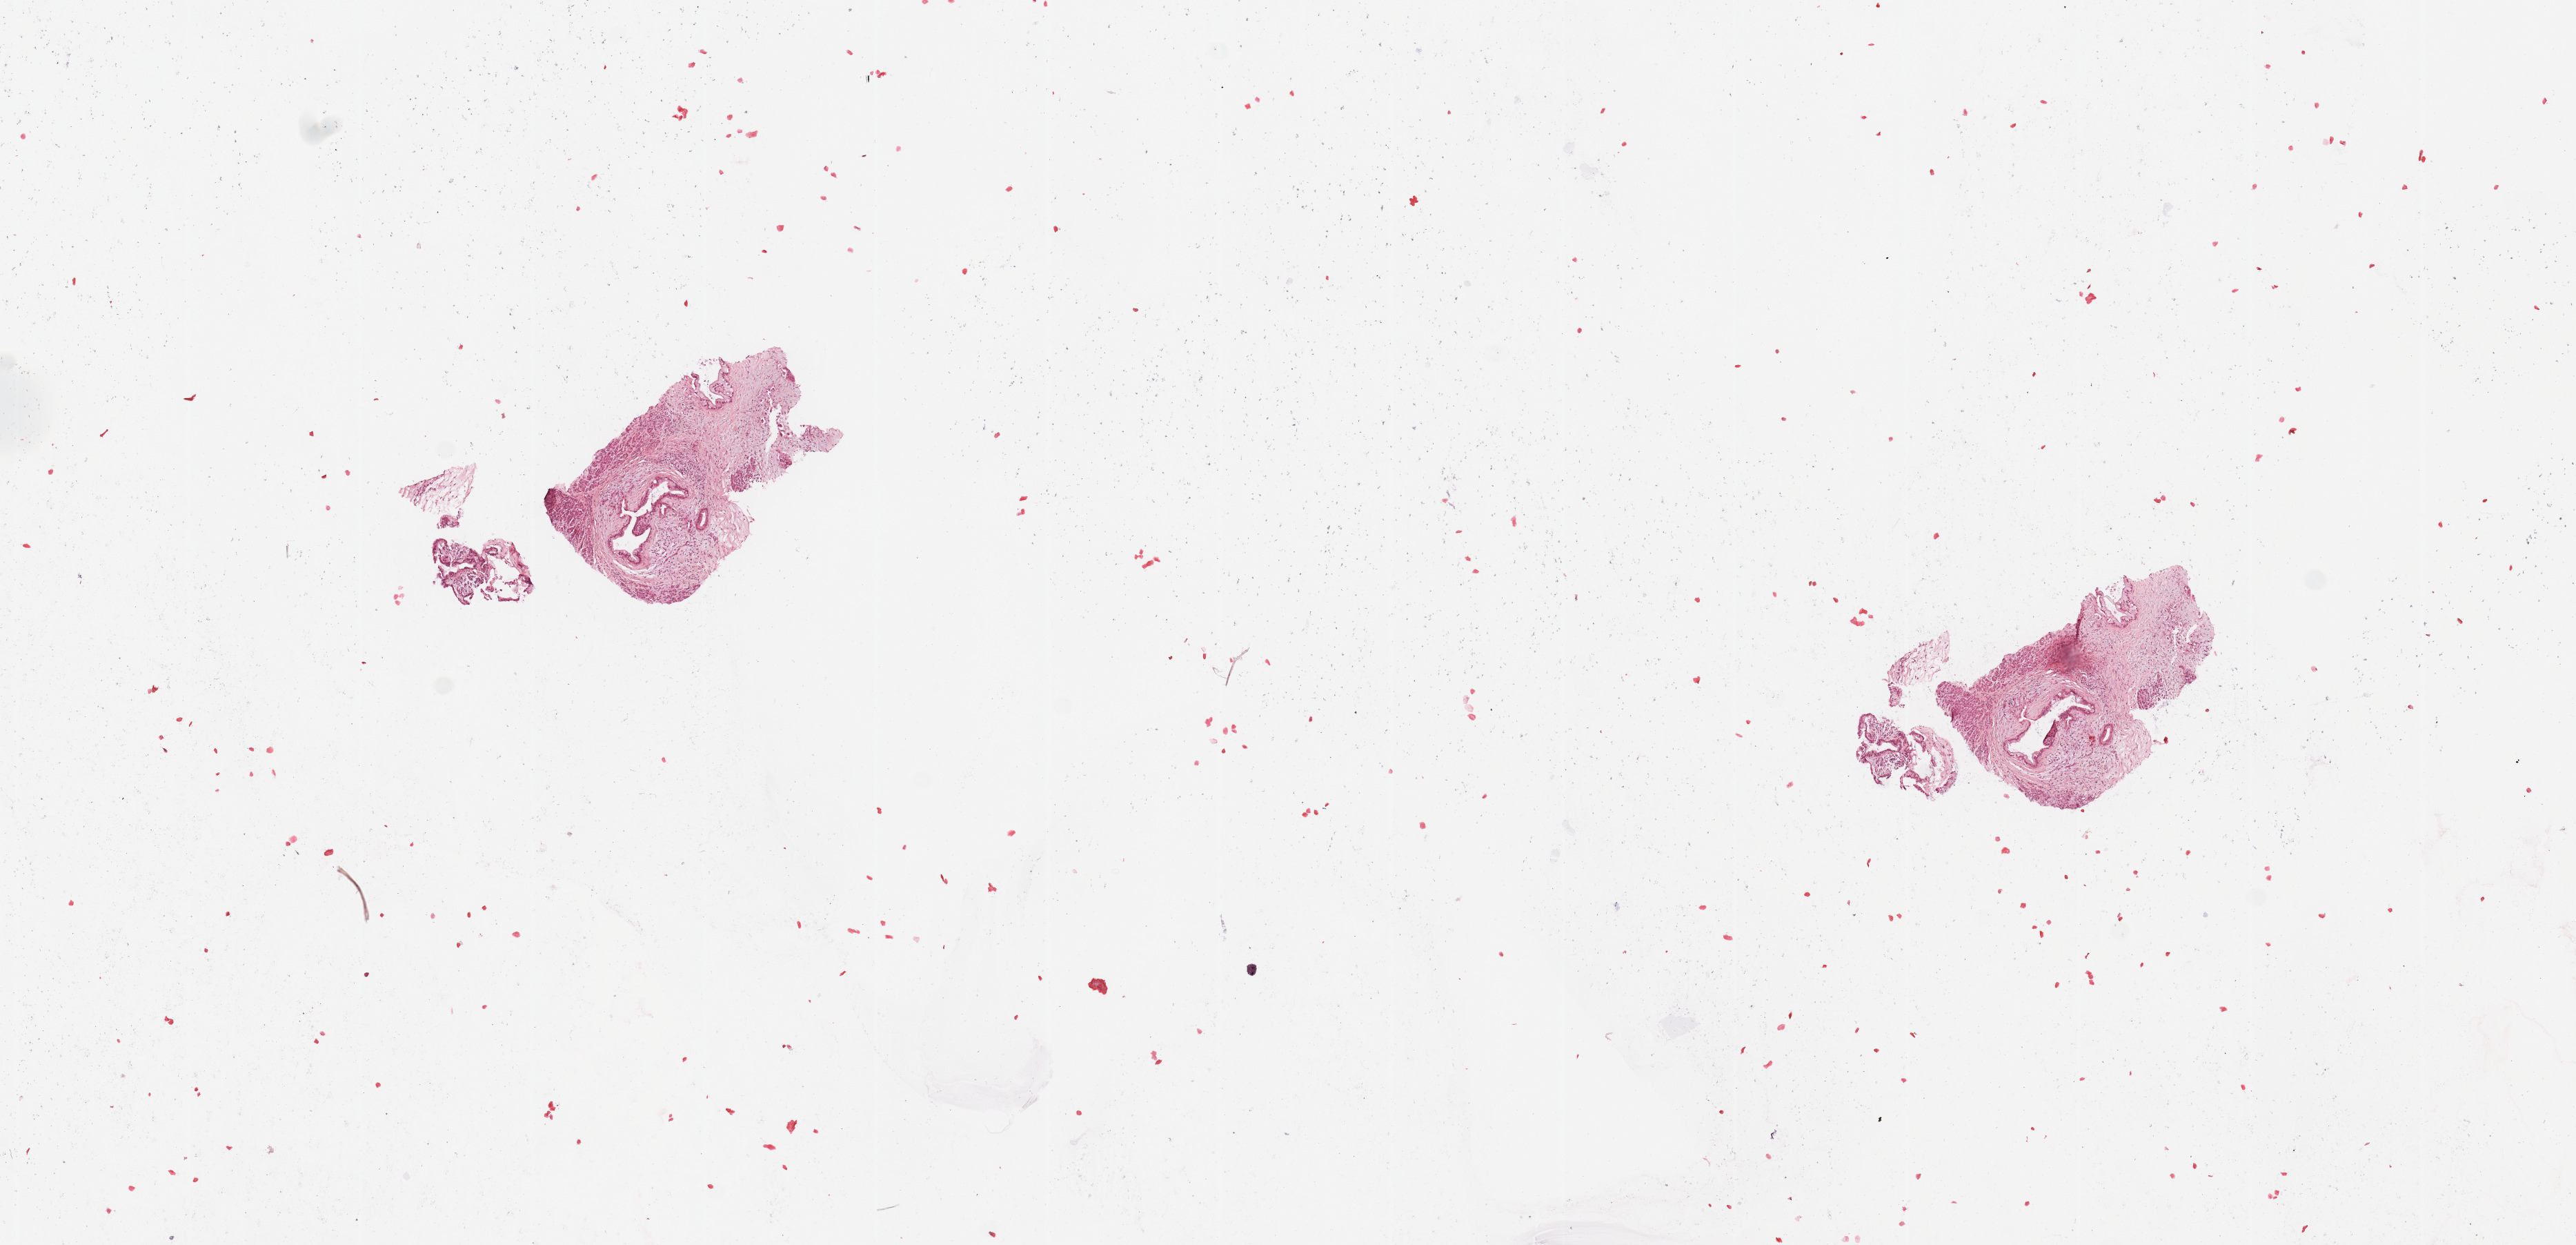
Digitized H&E tissue section (whole slide), low-resolution overview of the scanned area, about 14.8 x 7.1 mm (from a 20x scan), tumour tissue sample, sampled site: pancreas. 42-year-old male patient. Histologic grade: G2 (moderately differentiated). Slide review estimates, as recorded: tumour nuclei 10%, necrosis 0%.
Diagnosis: Infiltrating duct carcinoma, NOS. Primary tumour site (as recorded): head. AJCC pathologic stage: IIB.